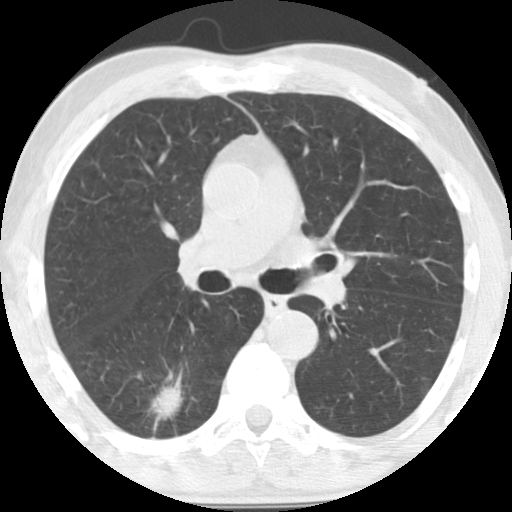
Low-dose screening chest CT, one axial slice. Position 85 of 135 along the scan axis. Reconstruction kernel STANDARD. 120 kVp. Lung window (W 1500 / L -600 HU). 2.5 mm slice thickness. 512 × 512 image matrix, field of view 300 × 300 mm.
Outlined on this slice (manually delineated by an expert):
- lesion 1 (tumor, lower lobe of right lung): bounding box <151,385,181,416> (left, top, right, bottom; pixels)